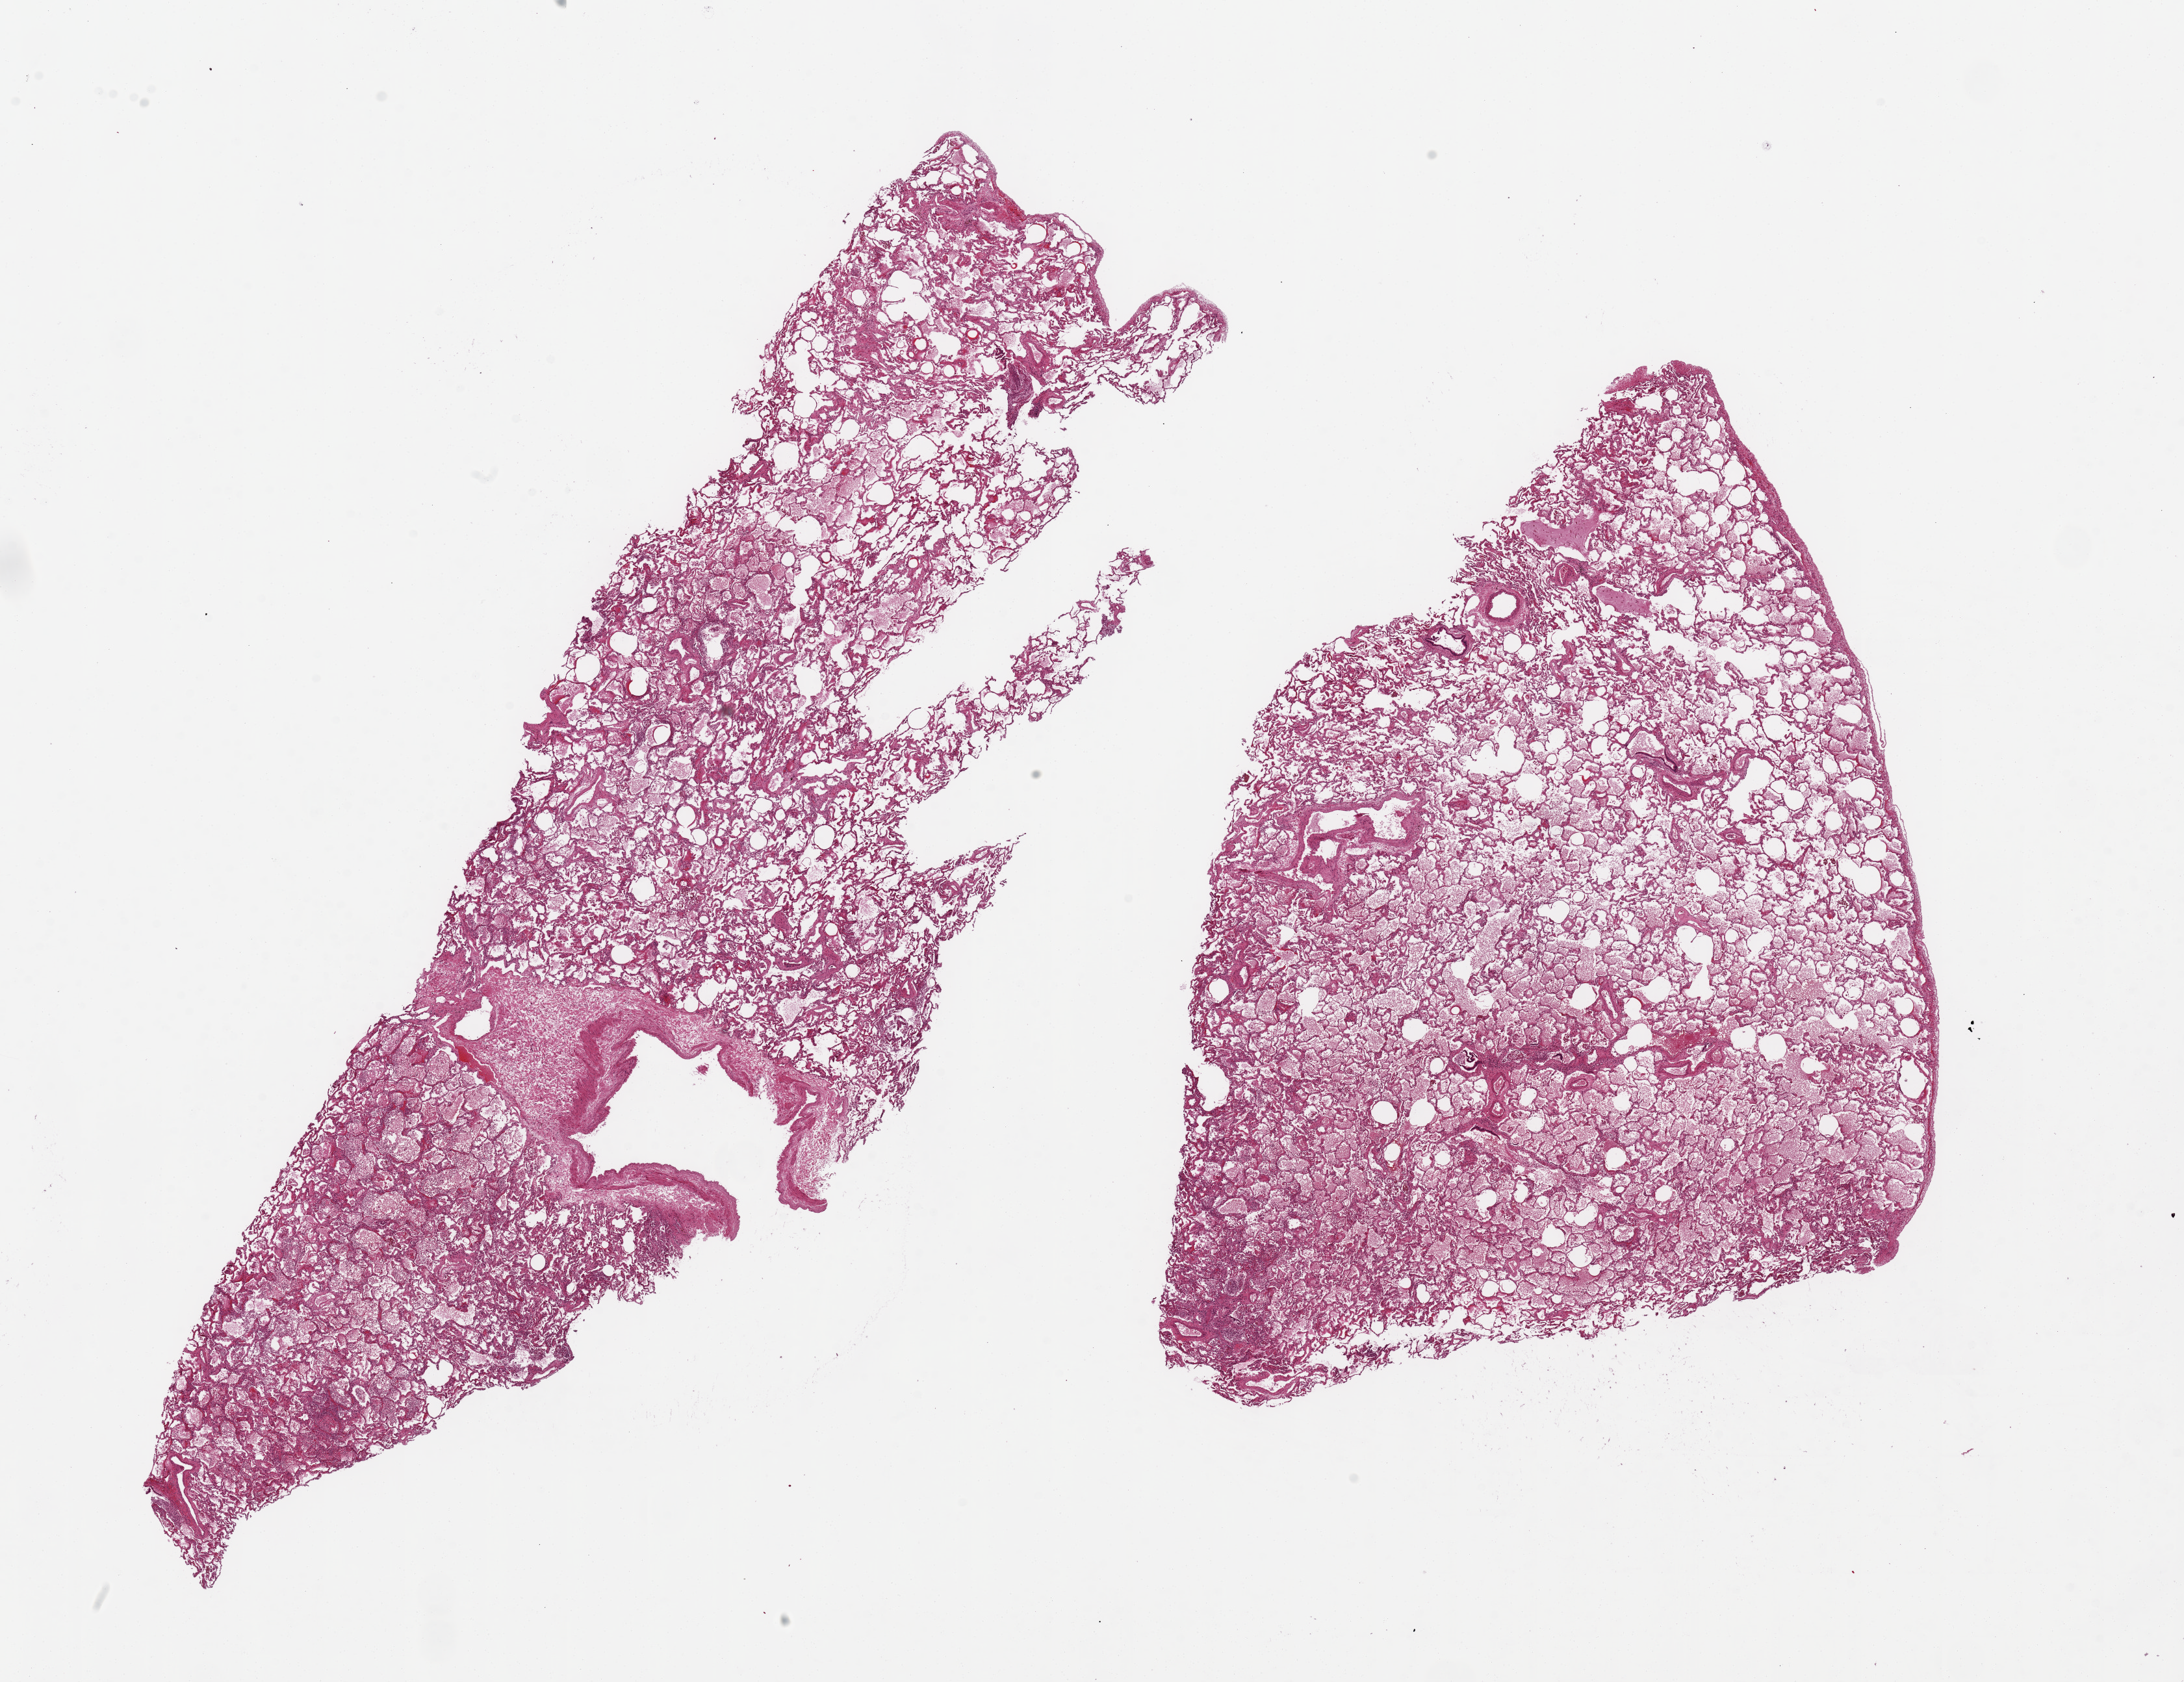
Whole-slide image, H&E stain, low-resolution overview of the scanned area, about 26.6 x 20.5 mm. PAXgene-fixed paraffin-embedded (PFPE) section. Target tissue: lung. Donor tissue sample.
Reviewer comment on this tissue sample: 2 pieces, 20x7 & 14x10mm; mild-moderate edmea/congestion.